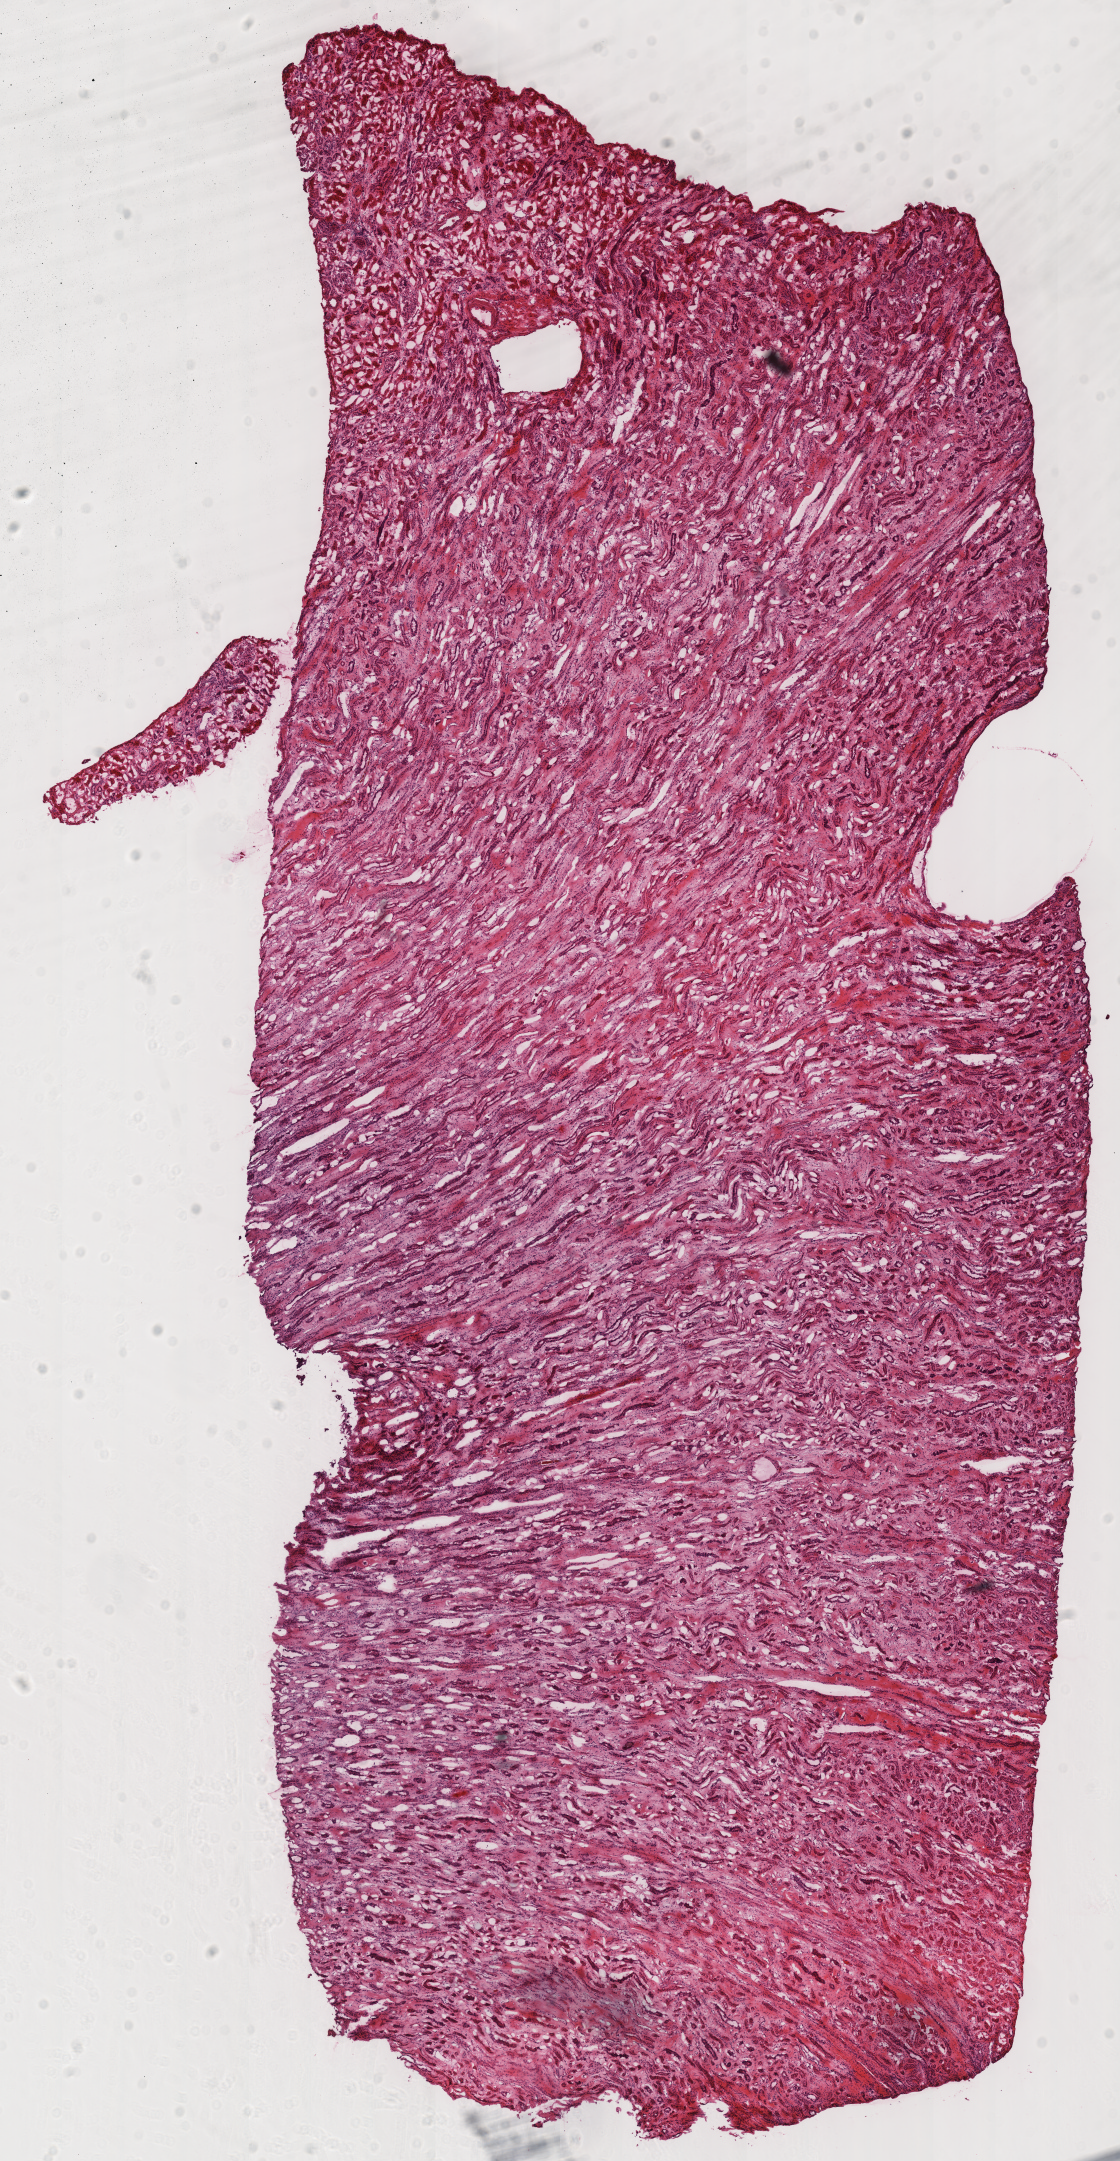
Digitized Hematoxylin and eosin (H&E) stained tissue section (whole slide) — low-resolution overview of the scanned area, about 8.8 x 17.0 mm (acquisition: 40x scan); frozen section; kidney, solid tissue normal (non-tumour tissue) sample. Patient: male, age at initial diagnosis 75 years. Inflammatory infiltration, as recorded: lymphocyte infiltration 0%, monocyte infiltration 0%, neutrophil infiltration 0%.
This section: solid tissue normal sample (biorepository sample class). Patient diagnosis: Renal cell carcinoma, chromophobe type.